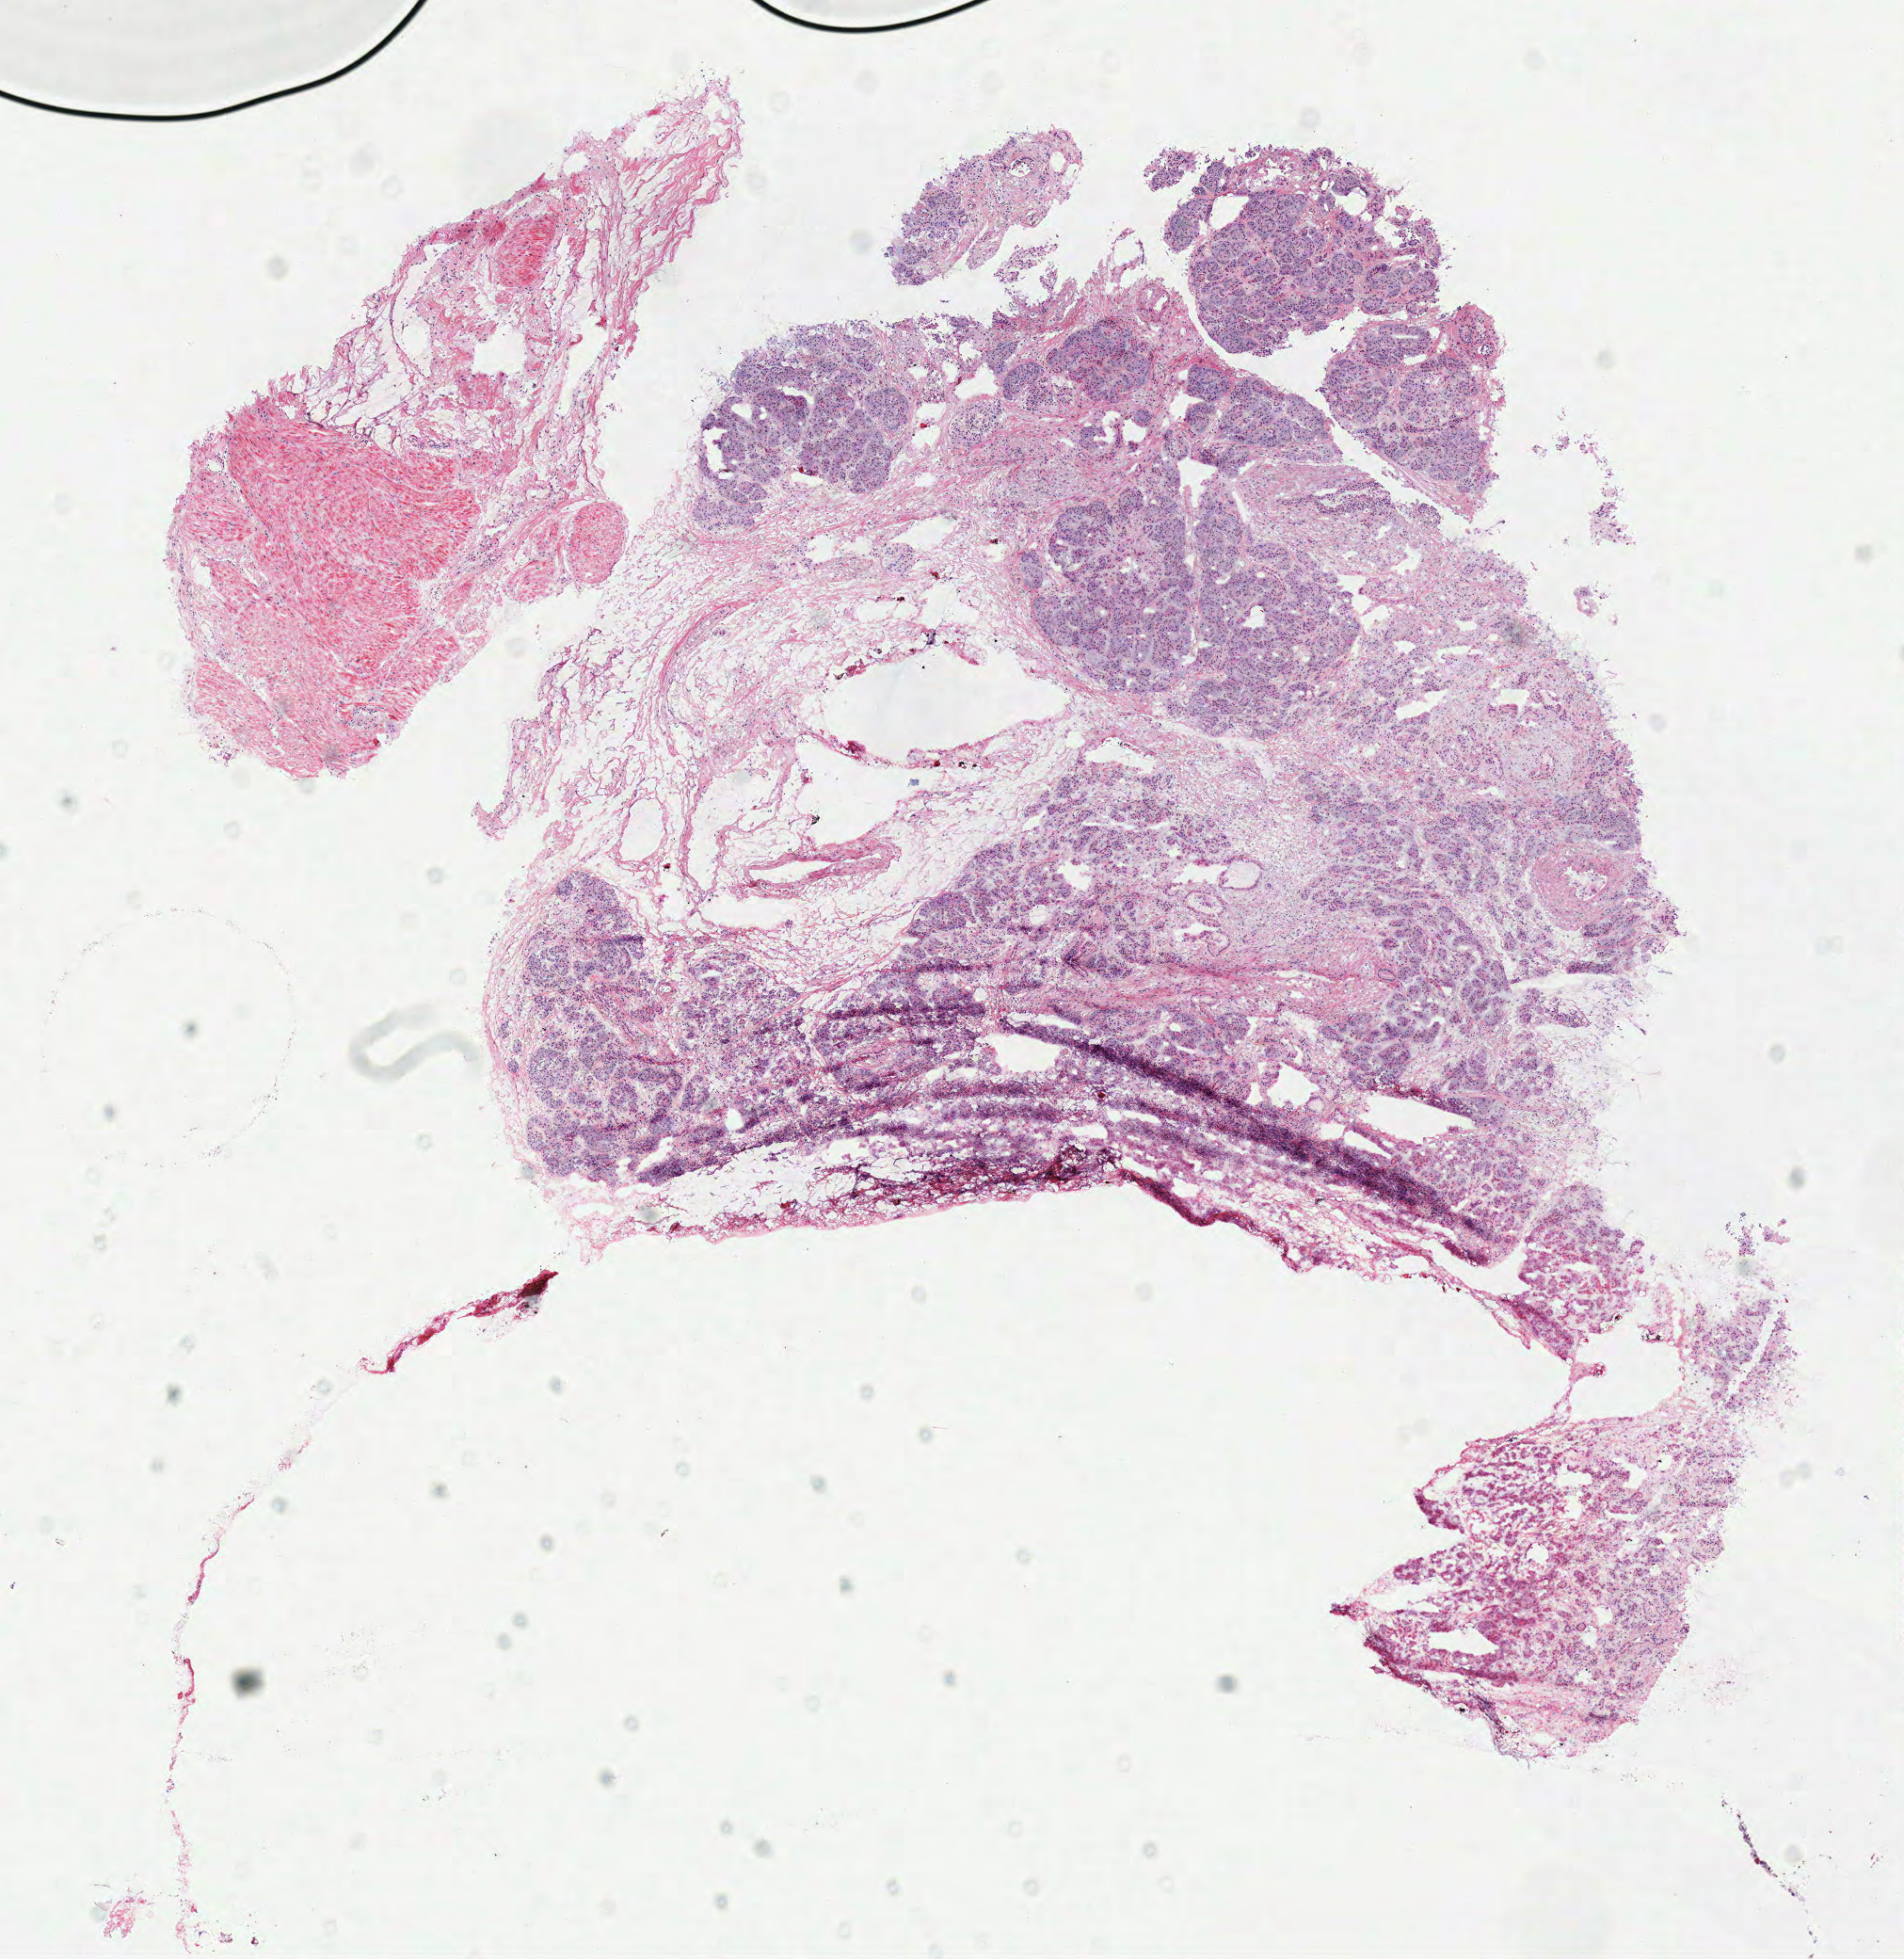
H&E-stained whole-slide image — shown as a low-resolution overview of the whole scanned area (about 8.0 x 8.2 mm, slide scanned at 40x). Frozen section from the top of the tissue portion. Solid tissue normal (non-tumour tissue) sample from the pancreas. Female, age 85 years at initial diagnosis.
* this section: solid tissue normal (non-tumour) sample from the same patient
* patient diagnosis: Infiltrating duct carcinoma, NOS (head of pancreas)